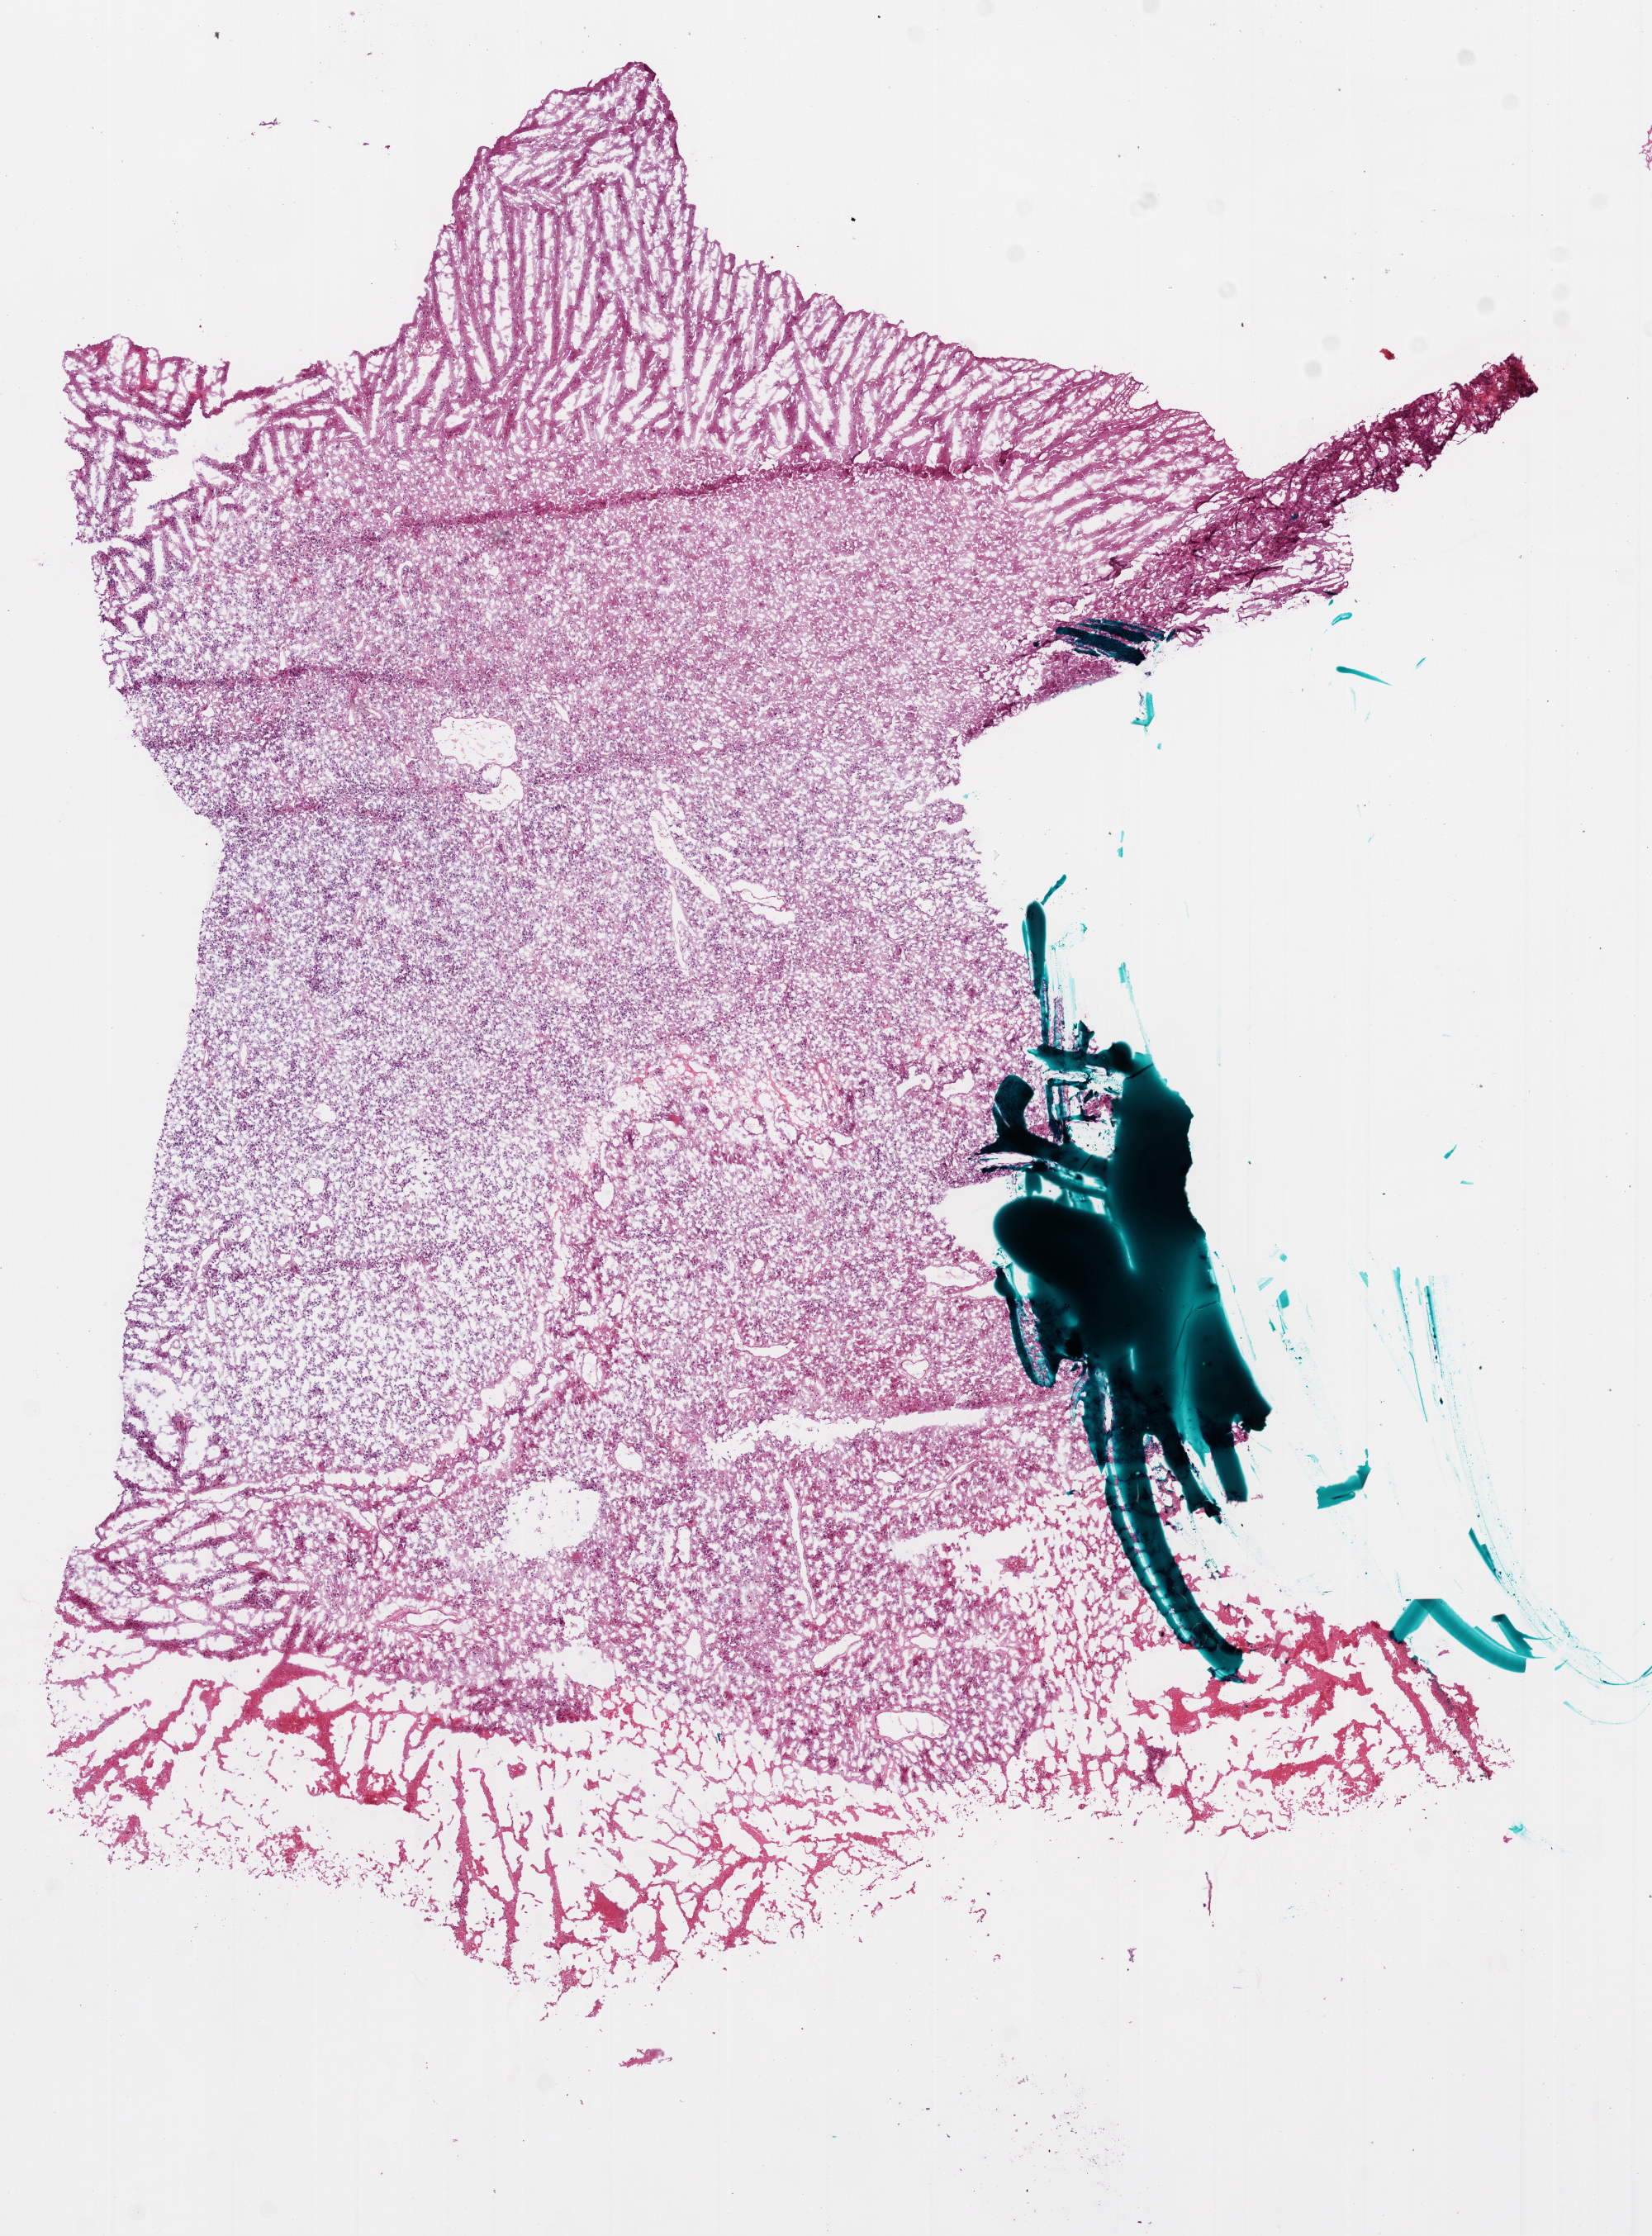
Whole-slide histology image, Hematoxylin and eosin (H&E) stained — a low-resolution overview of the entire scanned area, about 8.0 x 10.9 mm (from a 20x scan). Frozen section. Sample: primary tumour, brain. Patient: male, age at initial diagnosis 62 years. Slide review estimates, as recorded: tumour cells 75%, tumour nuclei 95%, normal cells 0%, stromal cells 10%, necrosis 15%. Infiltration values recorded for this section: lymphocyte infiltration 0%.
Histologic diagnosis: Glioblastoma.